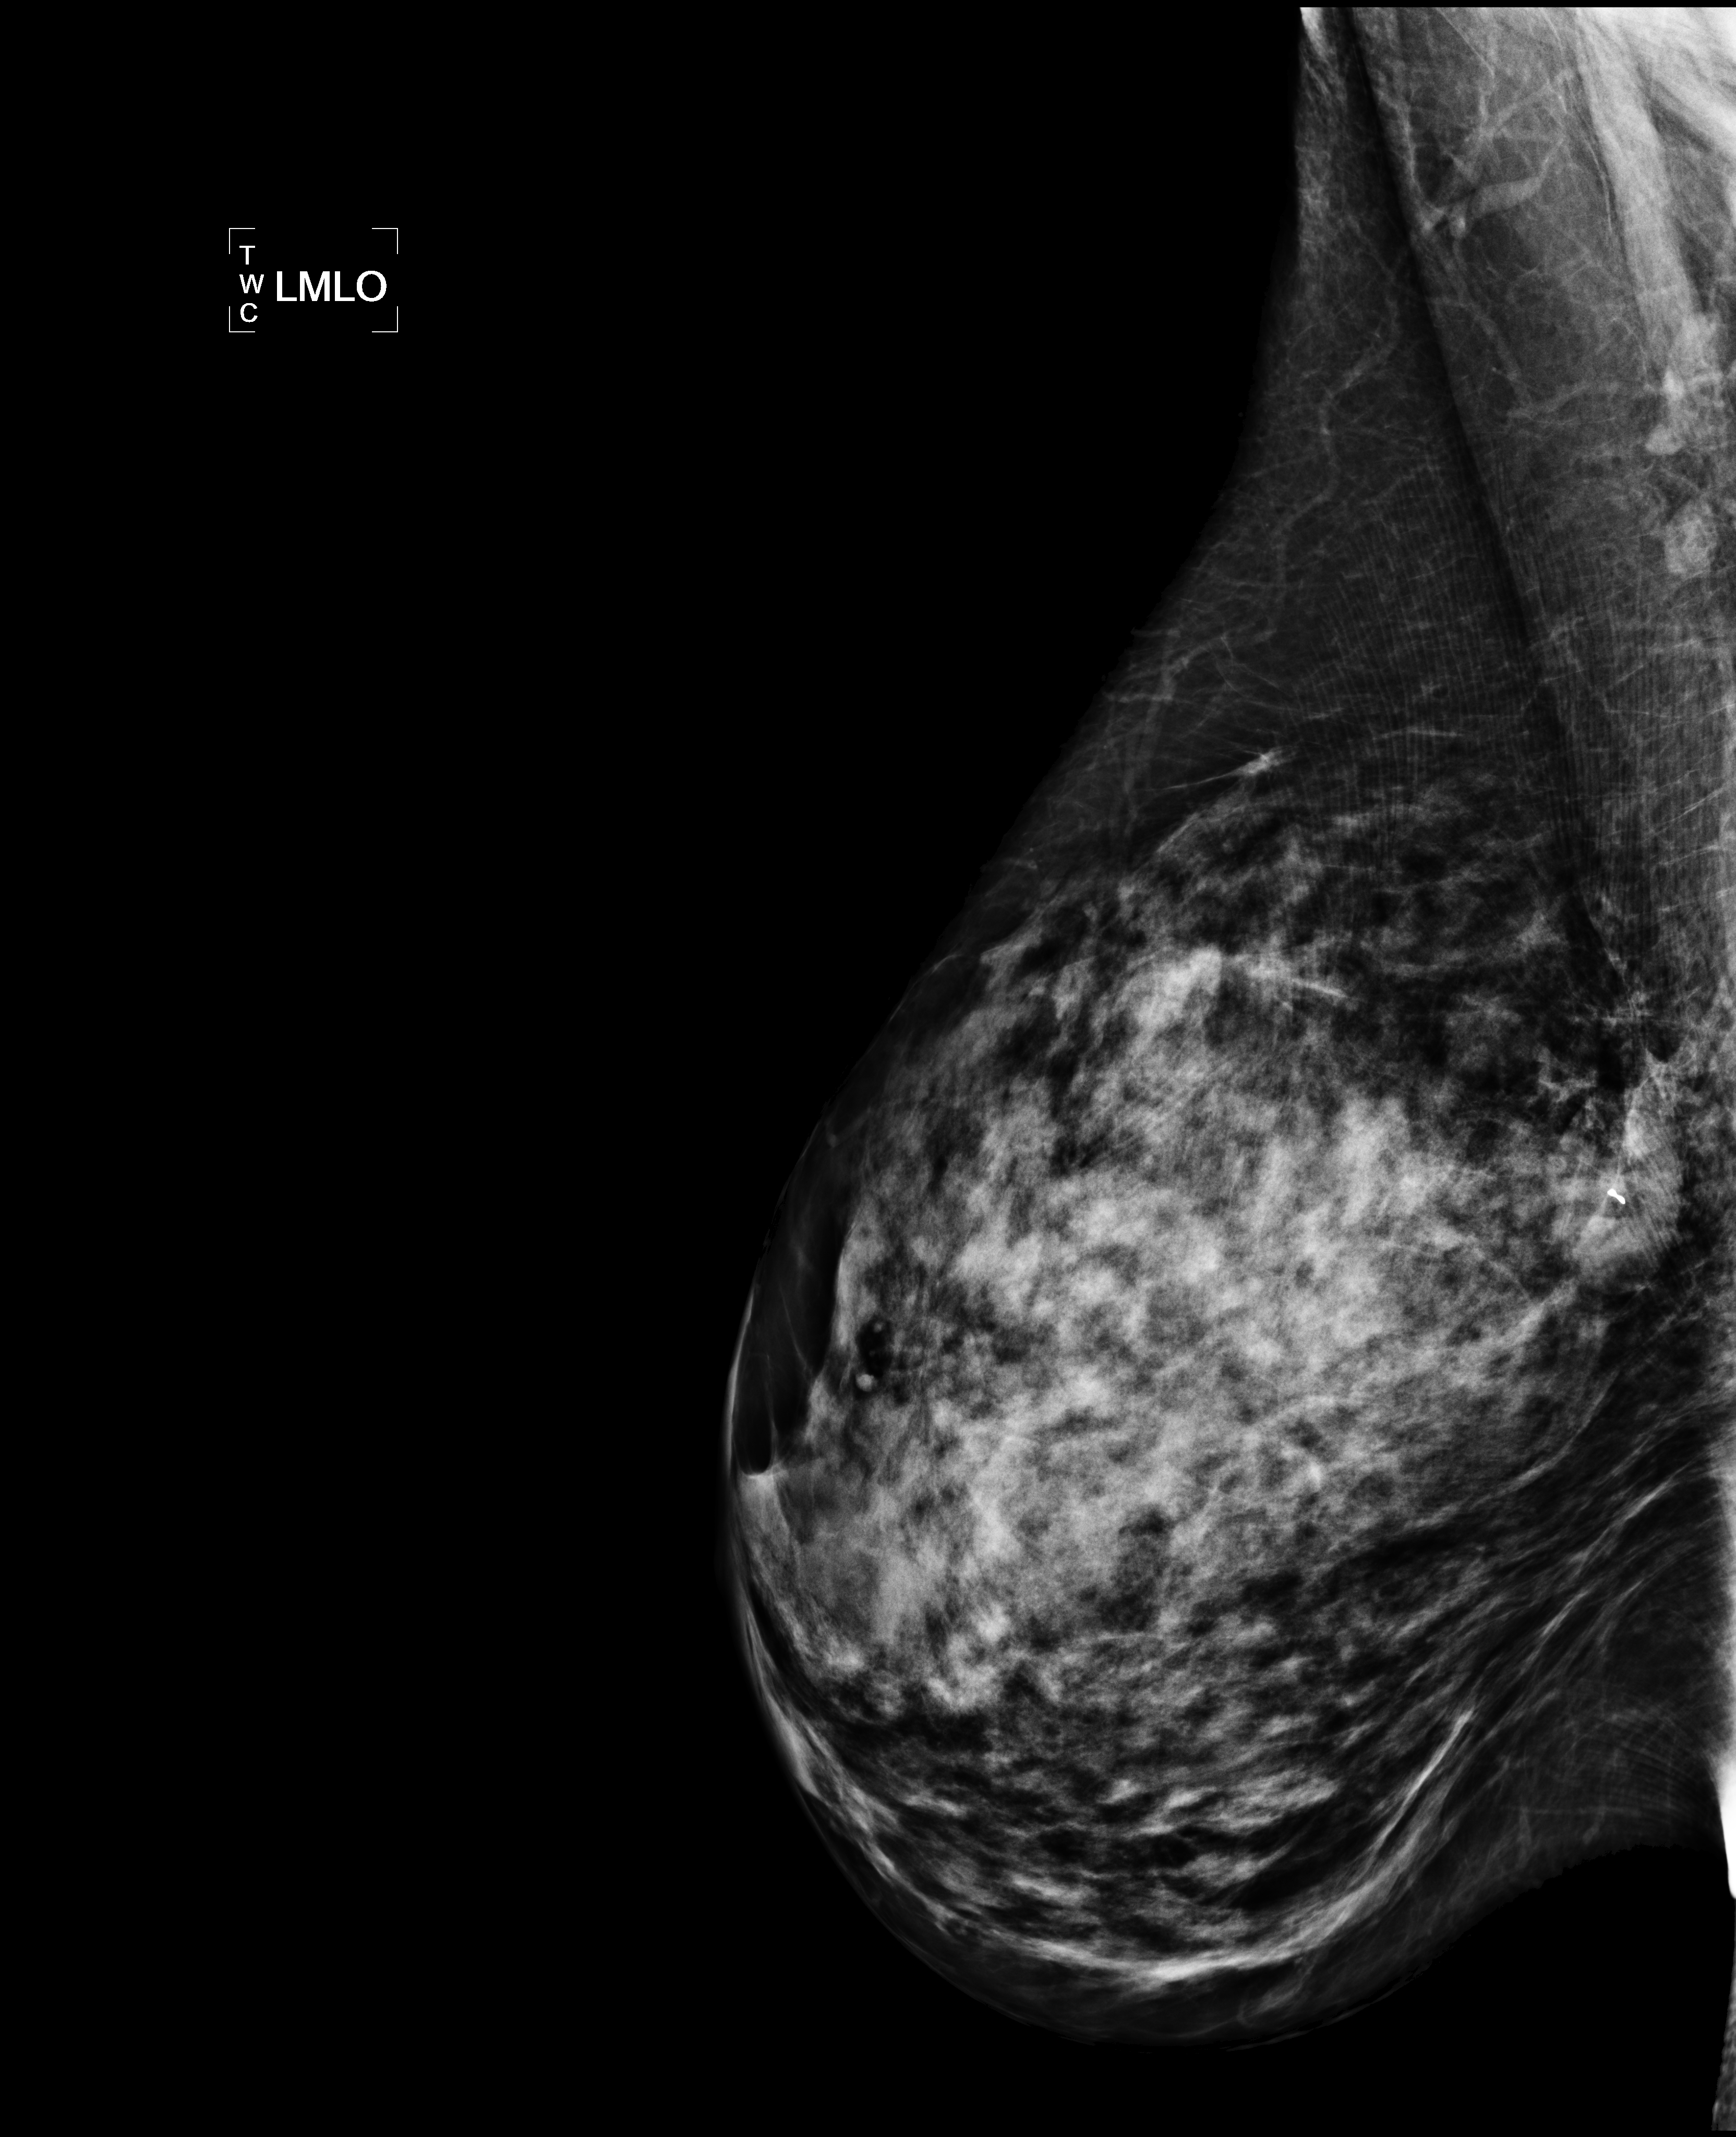
Diagnostic examination (additional views), system: Lorad Selenia. Patient: female, 43 years.
Image type: full-field digital mammogram. Breast: left. Projection: MLO view.